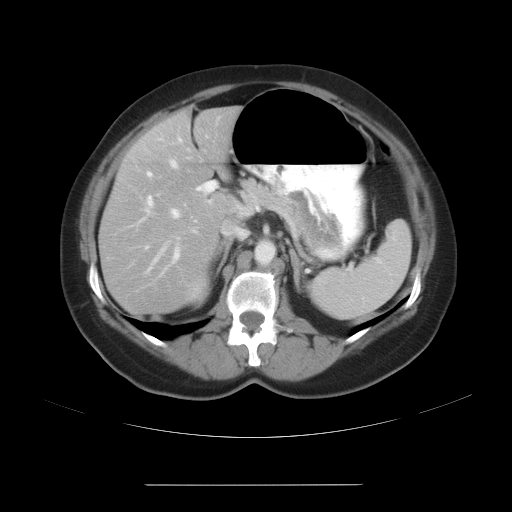
Contrast-enhanced abdominal CT, one axial slice; position 17 of 27 along the scan axis; reconstruction kernel STANDARD; 120 kVp; intravenous contrast given; soft-tissue window (W 400 / L 40 HU); 7.5 mm slice thickness; 512 × 512 image matrix, field of view 440 × 440 mm. Female patient, age 58 years. Case-level facts recorded for this patient, not image findings: diagnosis: colorectal cancer liver metastases, imaged before liver resection; multiple liver metastases: yes; largest metastasis: 1.9 cm; chemotherapy before resection: yes.
Annotated regions visible in this slice (expert manual segmentation):
- hepatic veins: bounding box <164,159,198,245> (left, top, right, bottom; pixels)
- liver: <101,108,237,311>
- planned liver remnant (the part of the liver to remain after resection): <112,118,232,222>
- portal vein (with intrahepatic branches): <120,116,254,277>
- liver metastasis: <187,112,204,126>
- liver metastasis: <188,113,191,118>